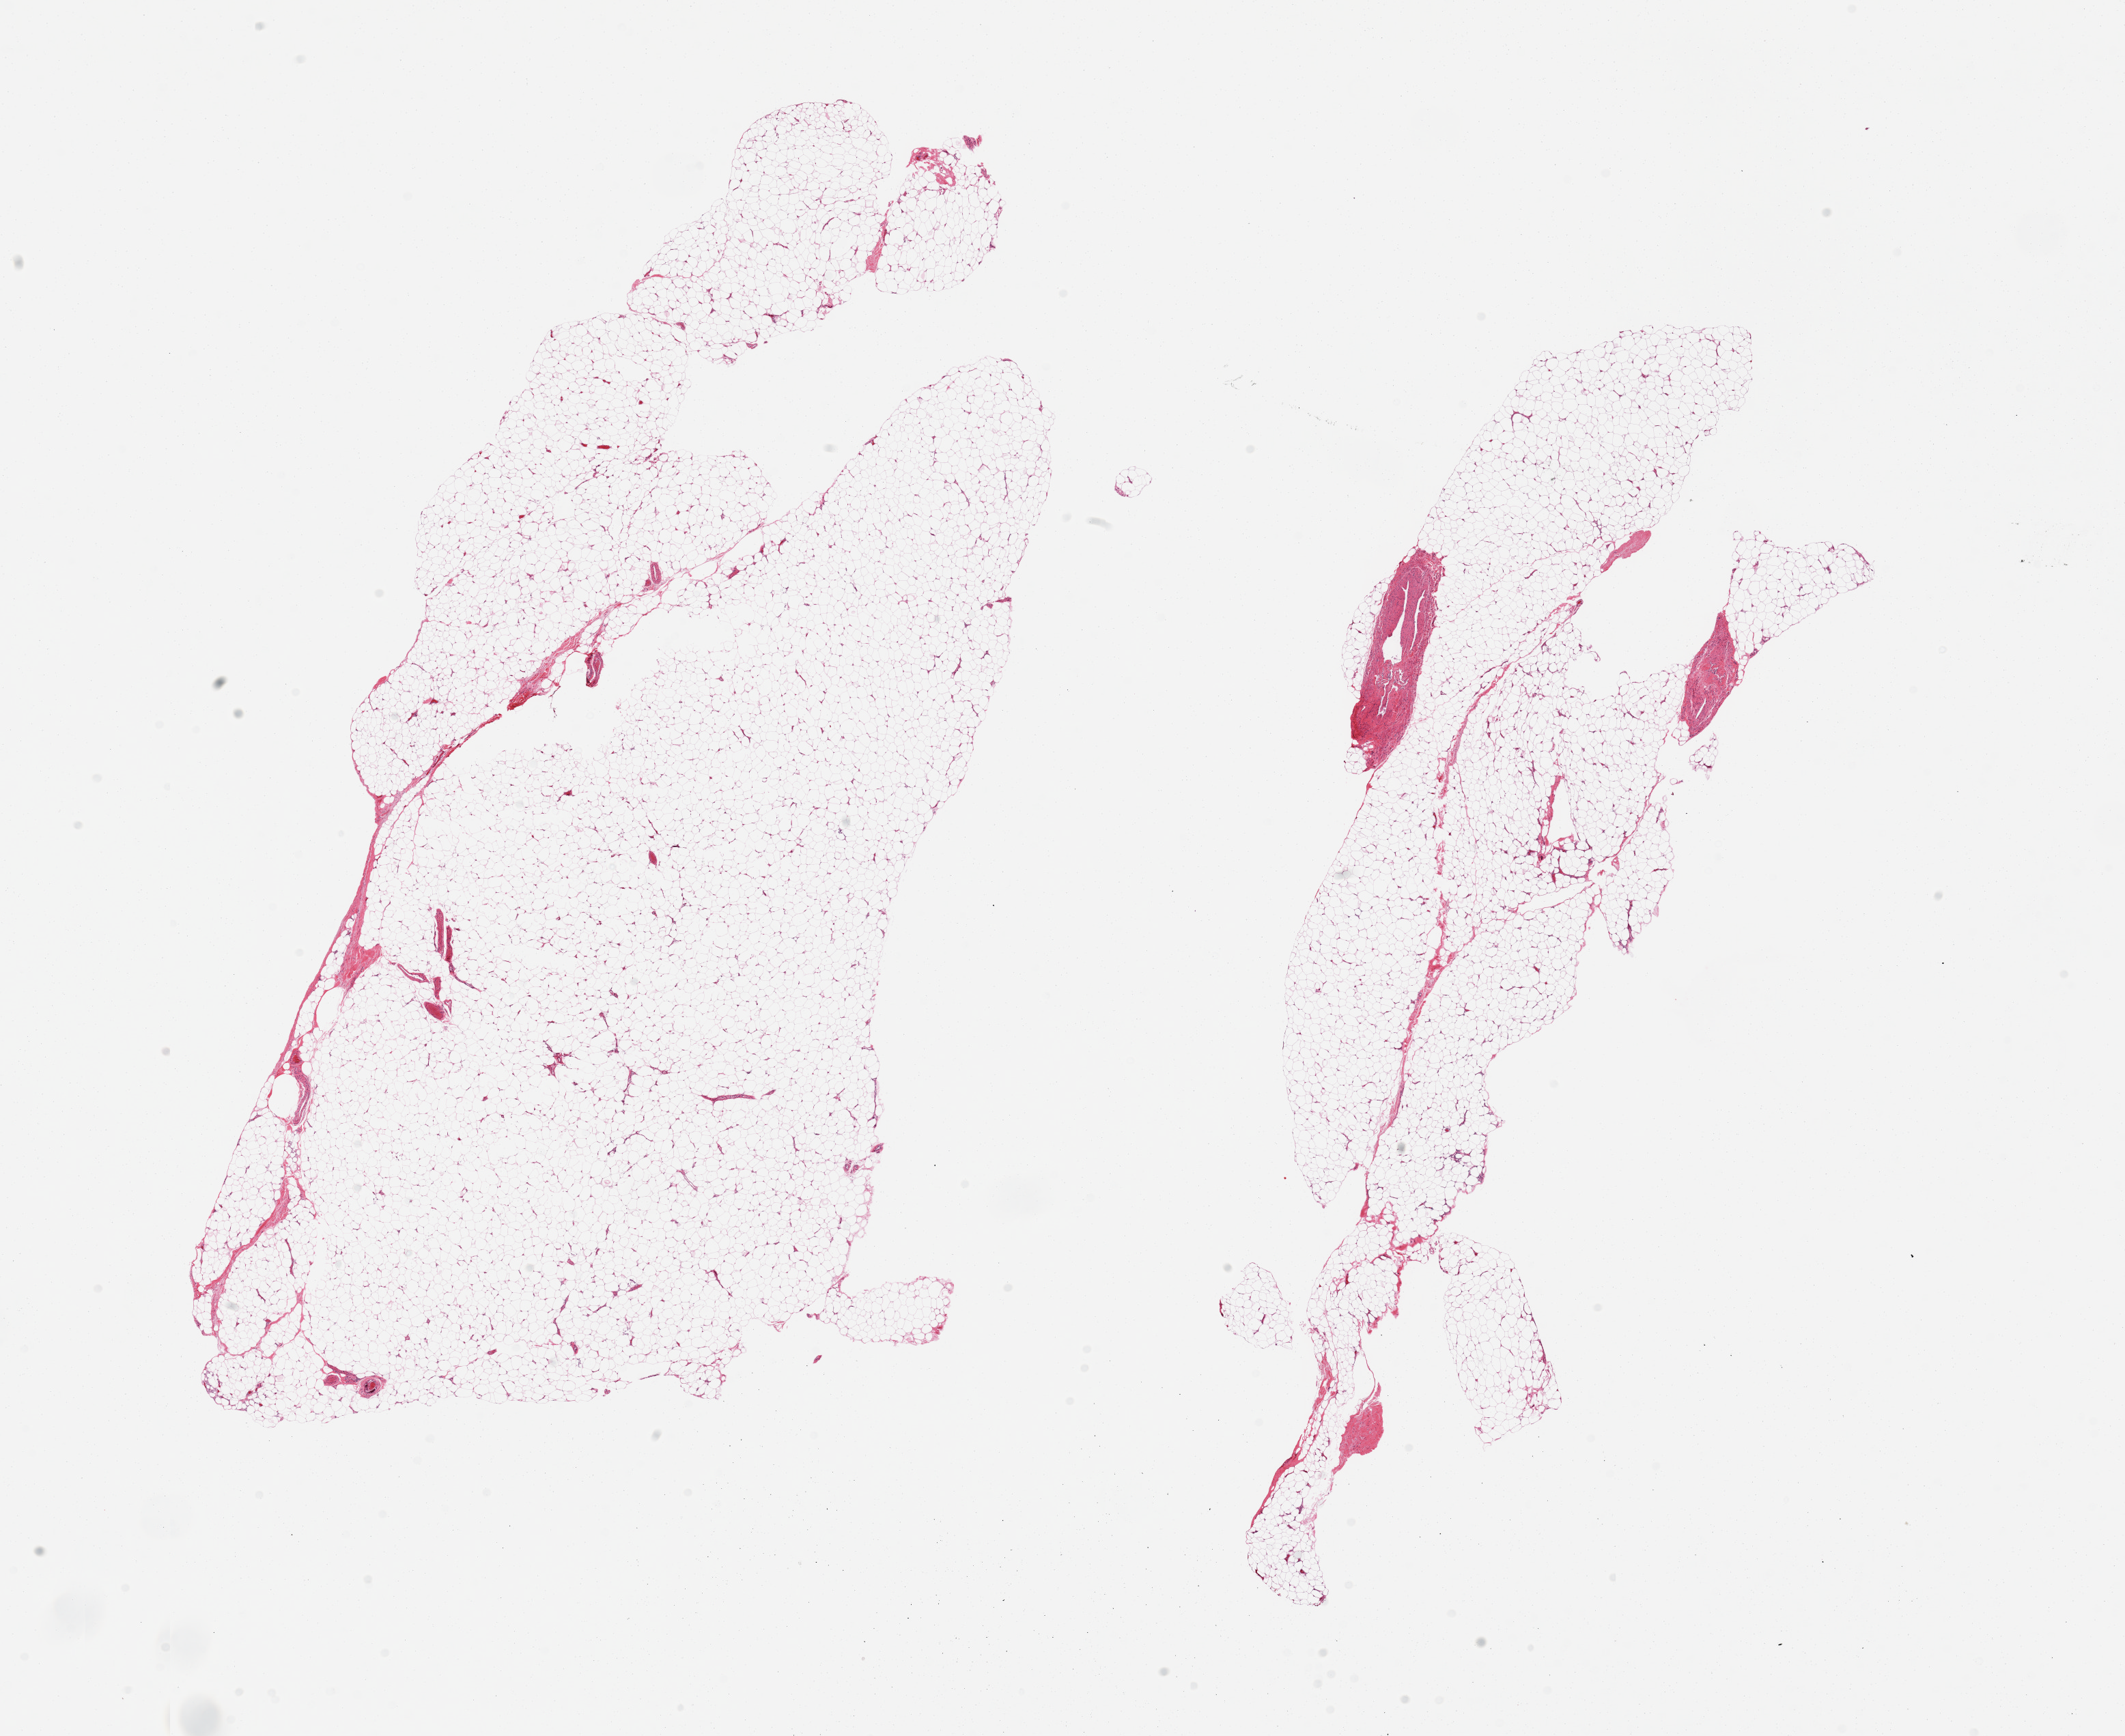
Hematoxylin and eosin (H&E) whole-slide image, brightfield — whole scanned area (about 24.6 x 20.1 mm) shown as a low-resolution overview; PAXgene-fixed paraffin-embedded (PFPE) section; target tissue: adipose tissue; donor tissue sample.
* review note (as recorded): 2 pieces, ~5% fibrovascular tissue